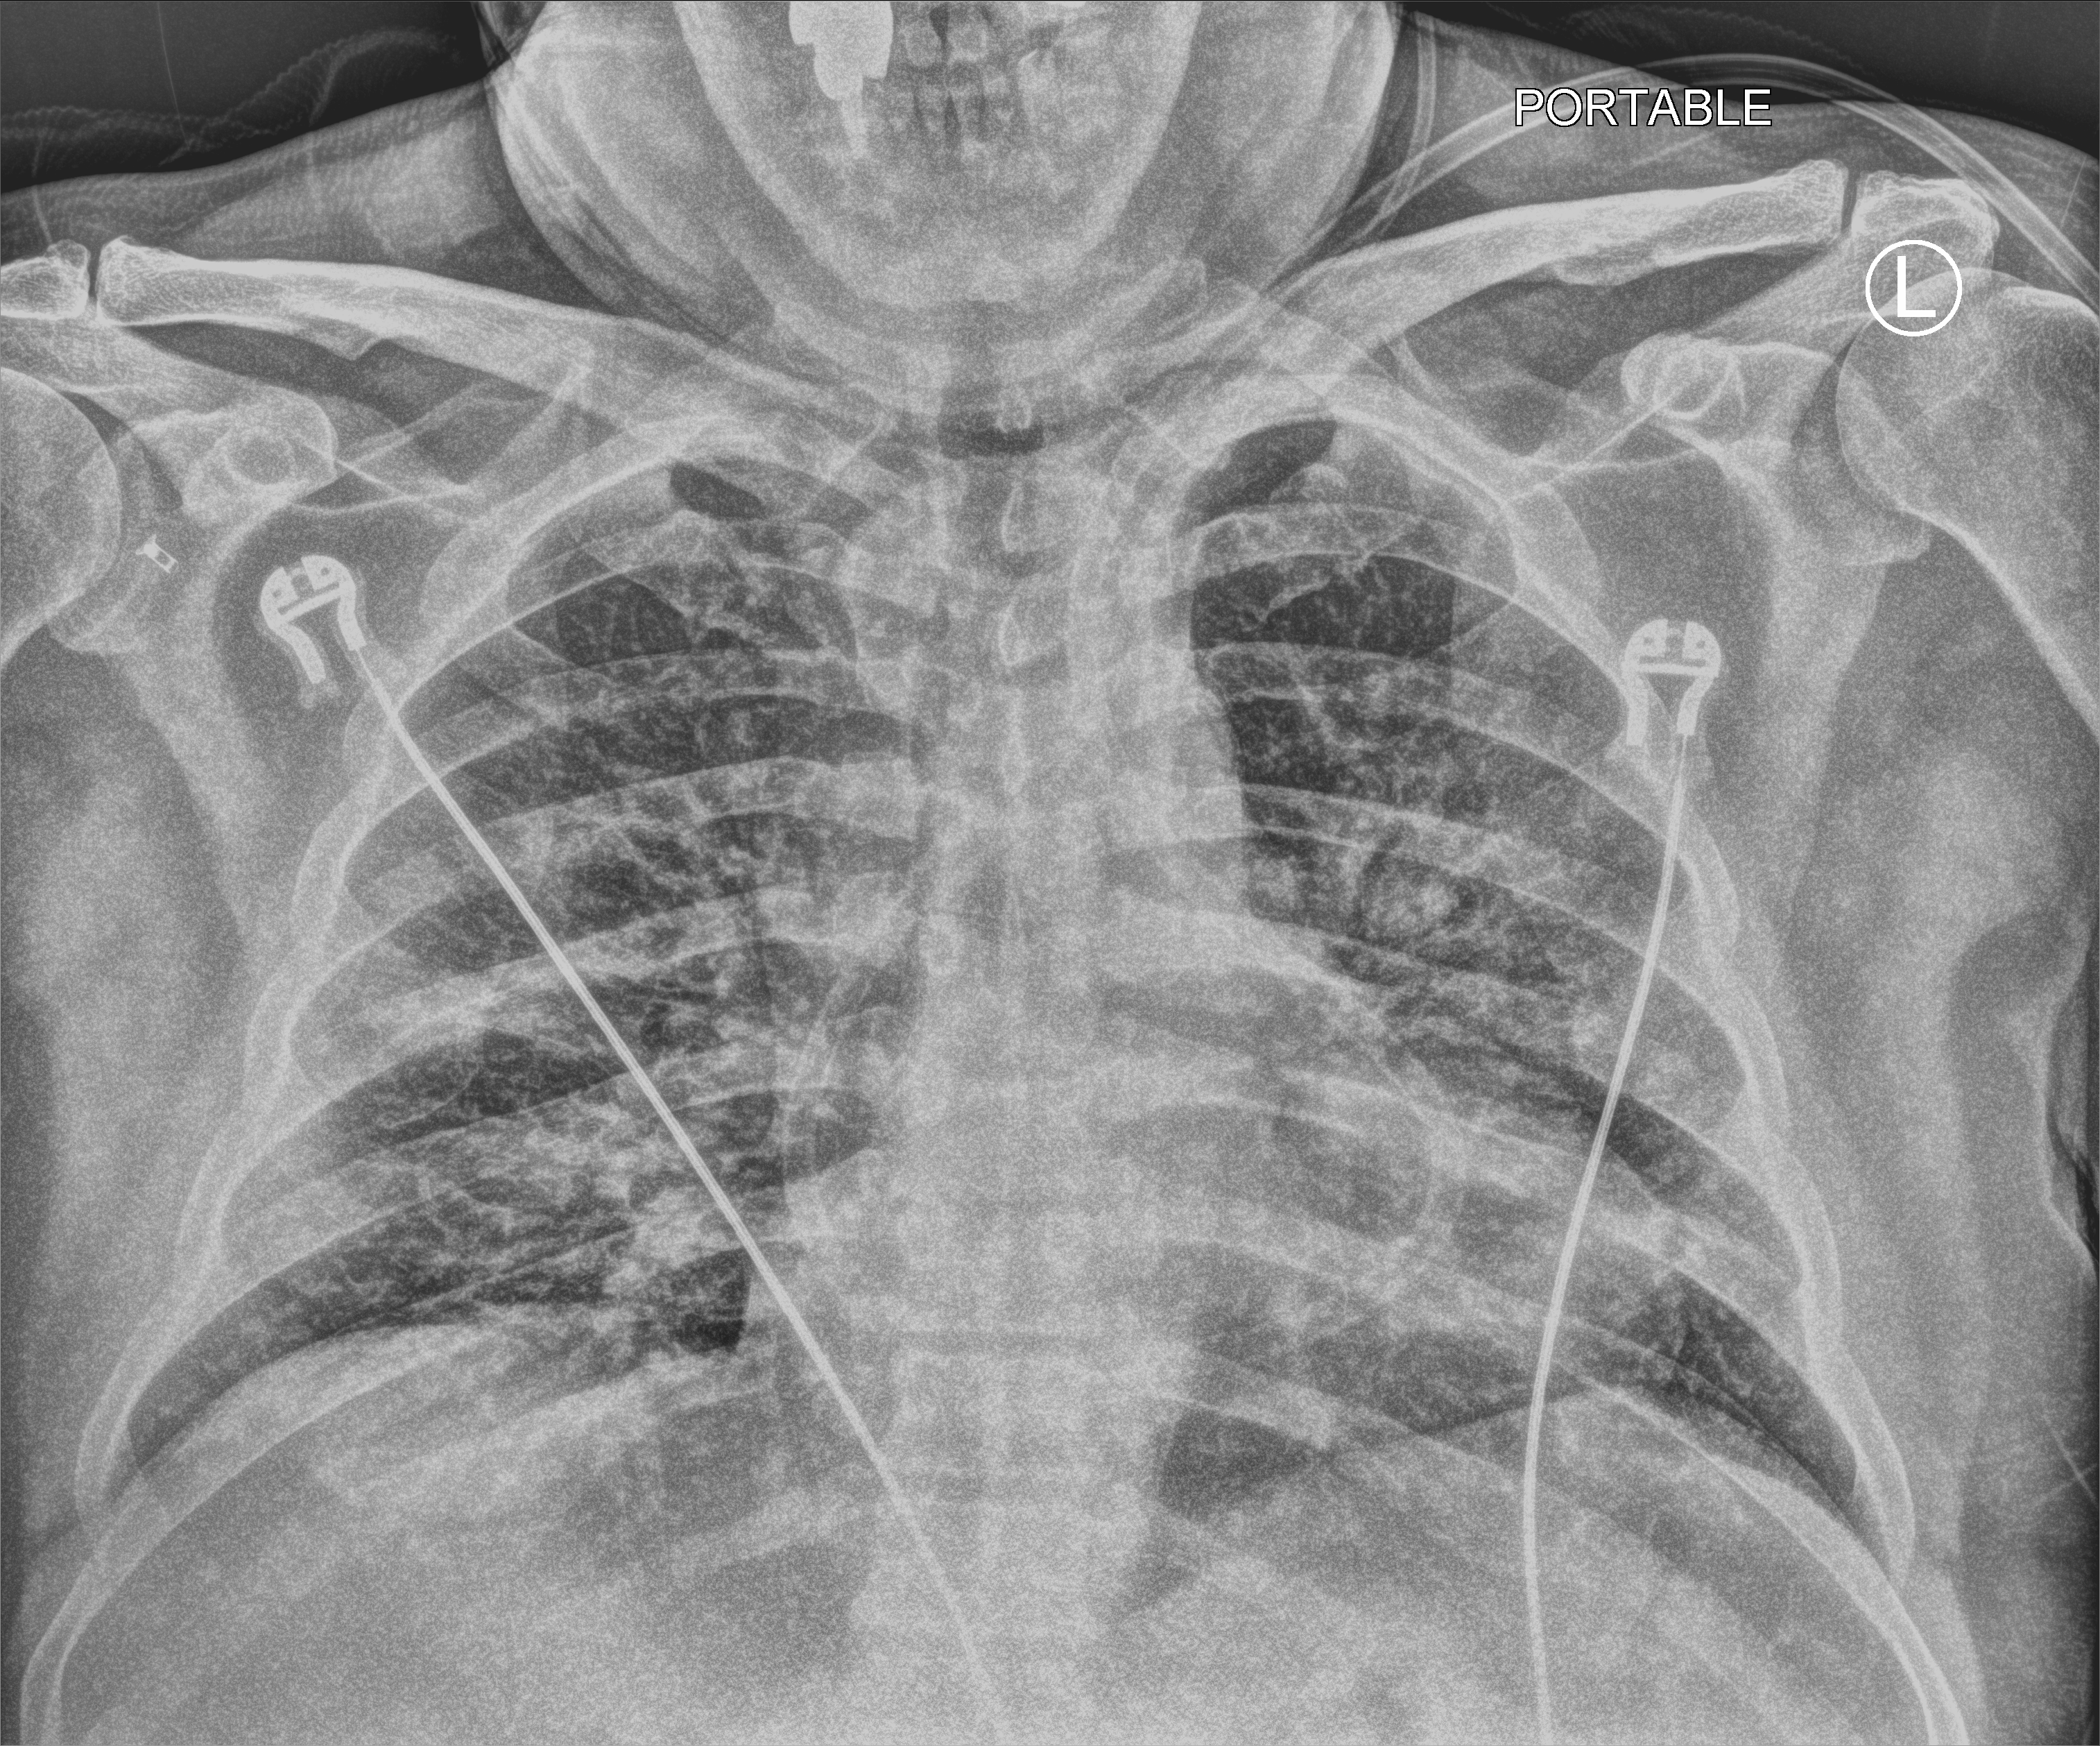
Bedside chest radiograph (computed radiography), anteroposterior (AP) projection. Patient hospitalised with COVID-19; male, aged 18–59 years.
From the hospital-stay record, not from the radiograph (when in the stay this image was taken is not recorded): mechanically ventilated during this hospital stay: yes; admitted to intensive care during this hospital stay: yes.